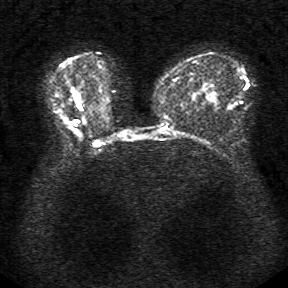
Breast MRI, one axial slice. Slice 17 of 34 in the series (ordered by position). Diffusion-weighted series; image 2 of 4 stored at this slice position (different b-values; order by instance number). 1.5 T. 5 mm slice thickness. 288 × 288 image matrix, field of view 340 × 340 mm. Female patient.
Structures marked on this image (outlined manually by an expert reader):
- tumour on diffusion-weighted imaging: bounding box (x1, y1, x2, y2) in pixels: (74, 97, 78, 101)